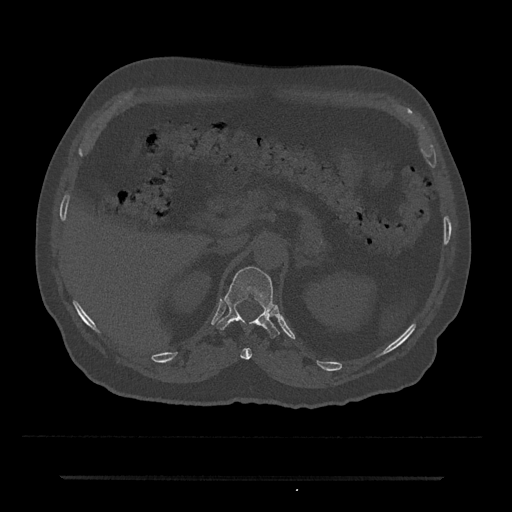
CT including the spine, one axial slice. Slice 138 of 797 in the series (ordered by position). 120 kVp. Bone window (W 1800 / L 400 HU). 0.5 mm slice thickness. 512 × 512 image matrix, field of view 437 × 437 mm. Male patient, age 69 years. From the clinical record (not read from this slice): primary cancer: prostate.
Outlined on this slice (semi-automatic segmentation, software-assisted and operator-edited):
- T11 vertebra: bounding box (x1, y1, x2, y2) in pixels: (233, 320, 252, 360)
- T12 vertebra: (216, 267, 279, 338)